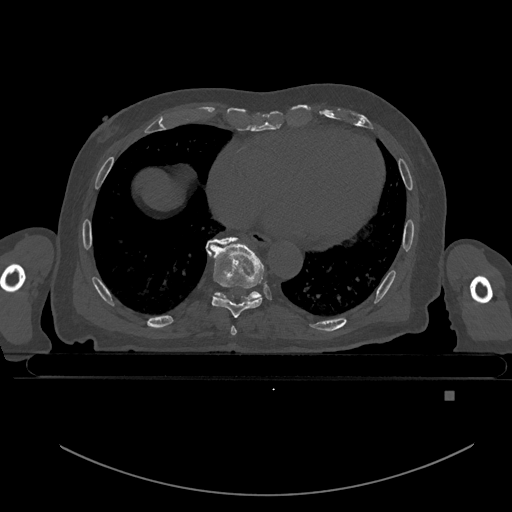
CT including the spine, one axial slice; slice 190 of 969 in the series (ordered by position); bone window (W 1800 / L 400 HU); 512 × 512 image matrix, field of view 456 × 456 mm. Patient: male, 82 years. Case-level facts recorded for this patient, not image findings: primary cancer: prostate; vertebrae with lytic lesions (as recorded): T11, T9, T8, T2.
Annotated regions visible in this slice (semi-automatically segmented with operator editing):
- T7 vertebra: bounding box [x1, y1, x2, y2] px = [231, 326, 237, 336]
- T8 vertebra: [208, 238, 264, 318]
- T9 vertebra: [206, 237, 262, 301]